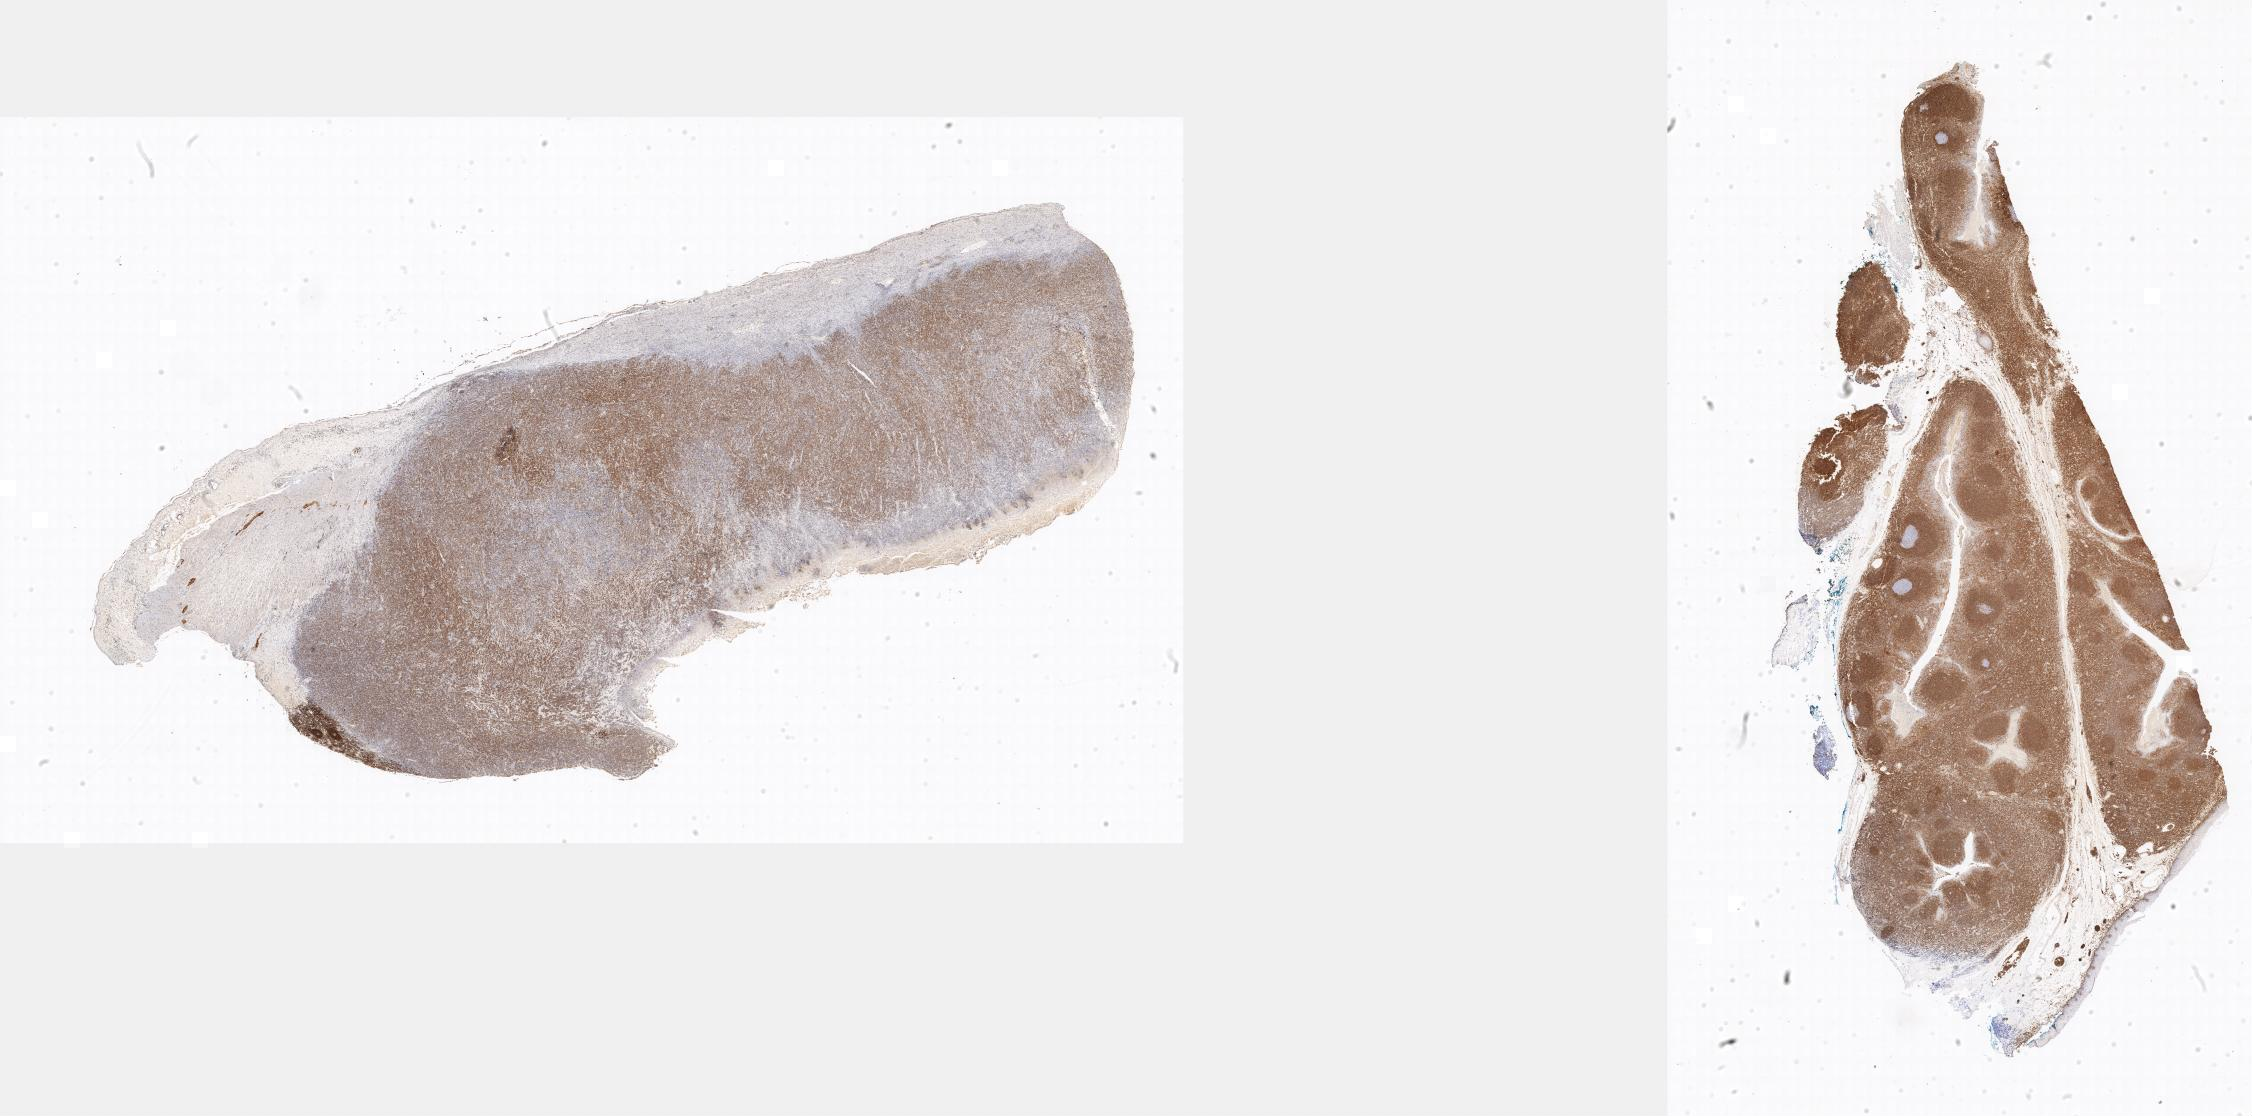
Immunohistochemistry (IHC) whole-slide image stained for BCL2 — low-resolution overview of the scanned area, specimen: tumor tissue, site: small intestine. Male, age 3 years at initial diagnosis.
Diagnosis: Burkitt lymphoma, NOS.